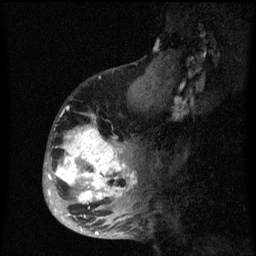
Breast MRI (dynamic contrast-enhanced), one sagittal slice; slice 24 of 60 in the series (ordered by position); dynamic contrast-enhanced series, image 2 of 3 at this slice position (ordered by acquisition); 1.5 T; TE 4.2 ms, TR 8 ms; 2 mm slice thickness; 256 × 256 image matrix, field of view 190 × 190 mm. Patient: female, 50 years.
Outlined on this slice (semi-automatic segmentation, software-assisted and operator-edited):
- analysis volume of interest (the breast-tissue region the enhancement analysis was run in; not a lesion): bounding box (x1, y1, x2, y2) in pixels: (43, 90, 142, 216)
- tumour enhancement mask (voxels above the 70 % enhancement threshold inside the analysis volume of interest): (48, 115, 137, 216)